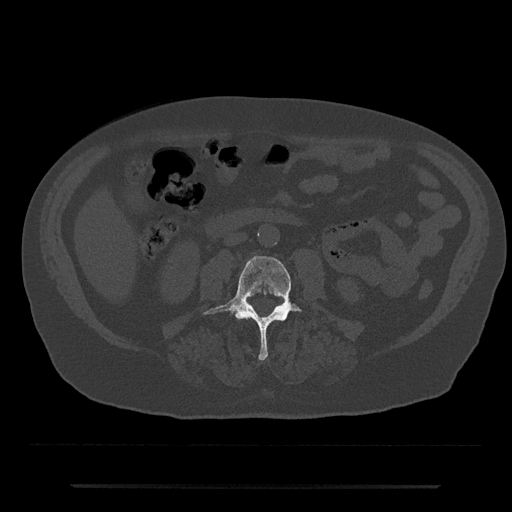
CT including the spine, one axial slice; position 409 of 797 along the scan axis; reconstruction kernel Br40s/3; 120 kVp; bone window (W 1800 / L 400 HU); 512 × 512 image matrix, field of view 434 × 434 mm. Patient: male, 80 years. From the clinical record (not read from this slice): primary cancer: prostate.
Annotated regions visible in this slice (semi-automatic segmentation, software-assisted and operator-edited):
- L3 vertebra: box from (x=204, y=256) to (x=301, y=361) px